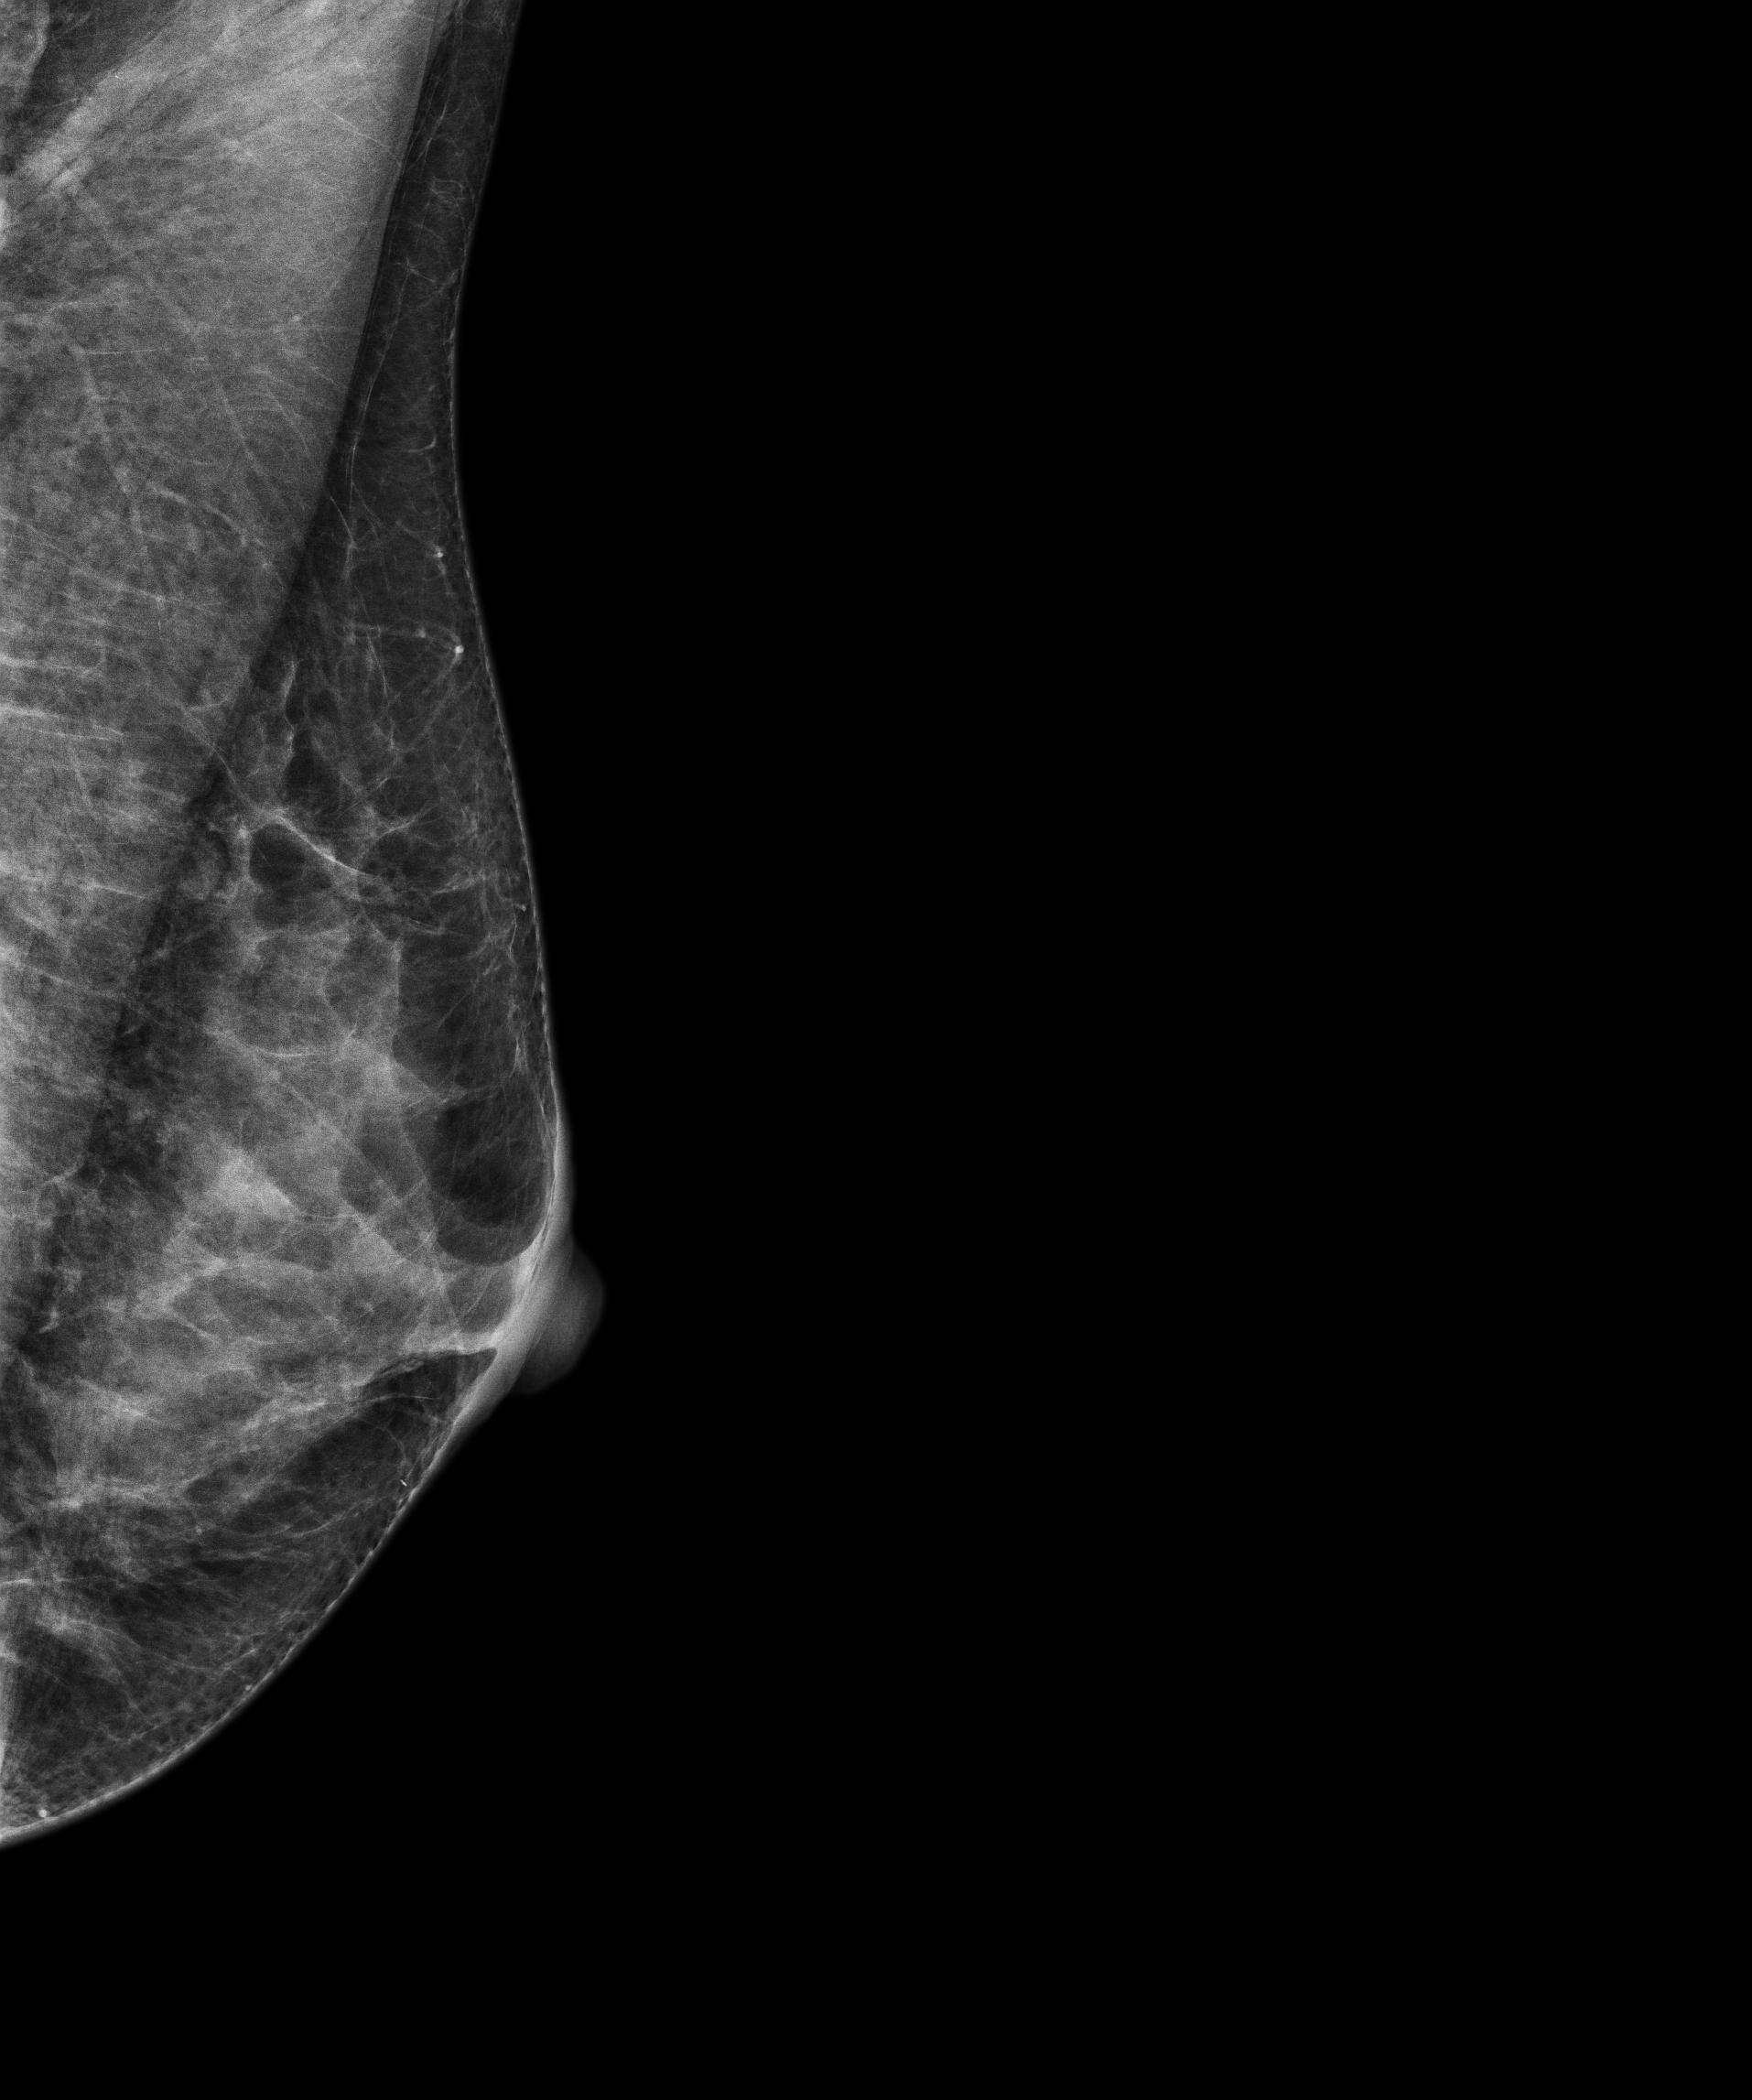
Screening examination. Female patient, age 47 years.
Image type: full-field digital mammogram. Breast: left. Projection: mediolateral oblique (MLO) view.